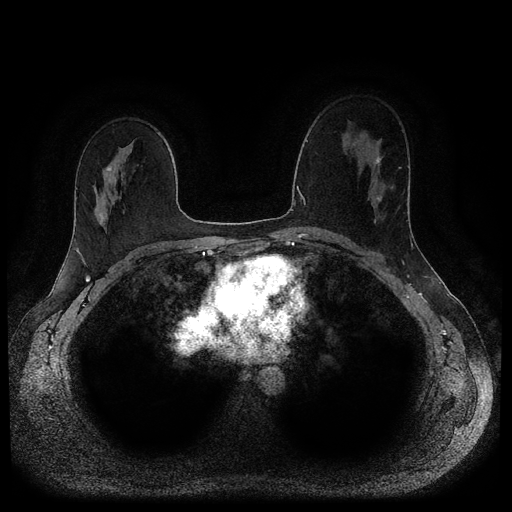
Breast MRI (dynamic contrast-enhanced, multi-phase), one axial slice. Position 62 of 116 along the scan axis. Dynamic contrast-enhanced series, time point 2 of 5 at this slice position (early post-contrast). 1.5 T. TE 2.6 ms, TR 5.3 ms. 2 mm slice thickness. 512 × 512 image matrix, field of view 350 × 350 mm. Female patient, age 45 years.
Structures marked on this image (semi-automatically segmented with operator editing):
- breast lesion (labelled 'tumour' in the annotation; benign lesions carry a separate 'benign' label): bounding box (x1, y1, x2, y2) in pixels: (375, 157, 383, 203)